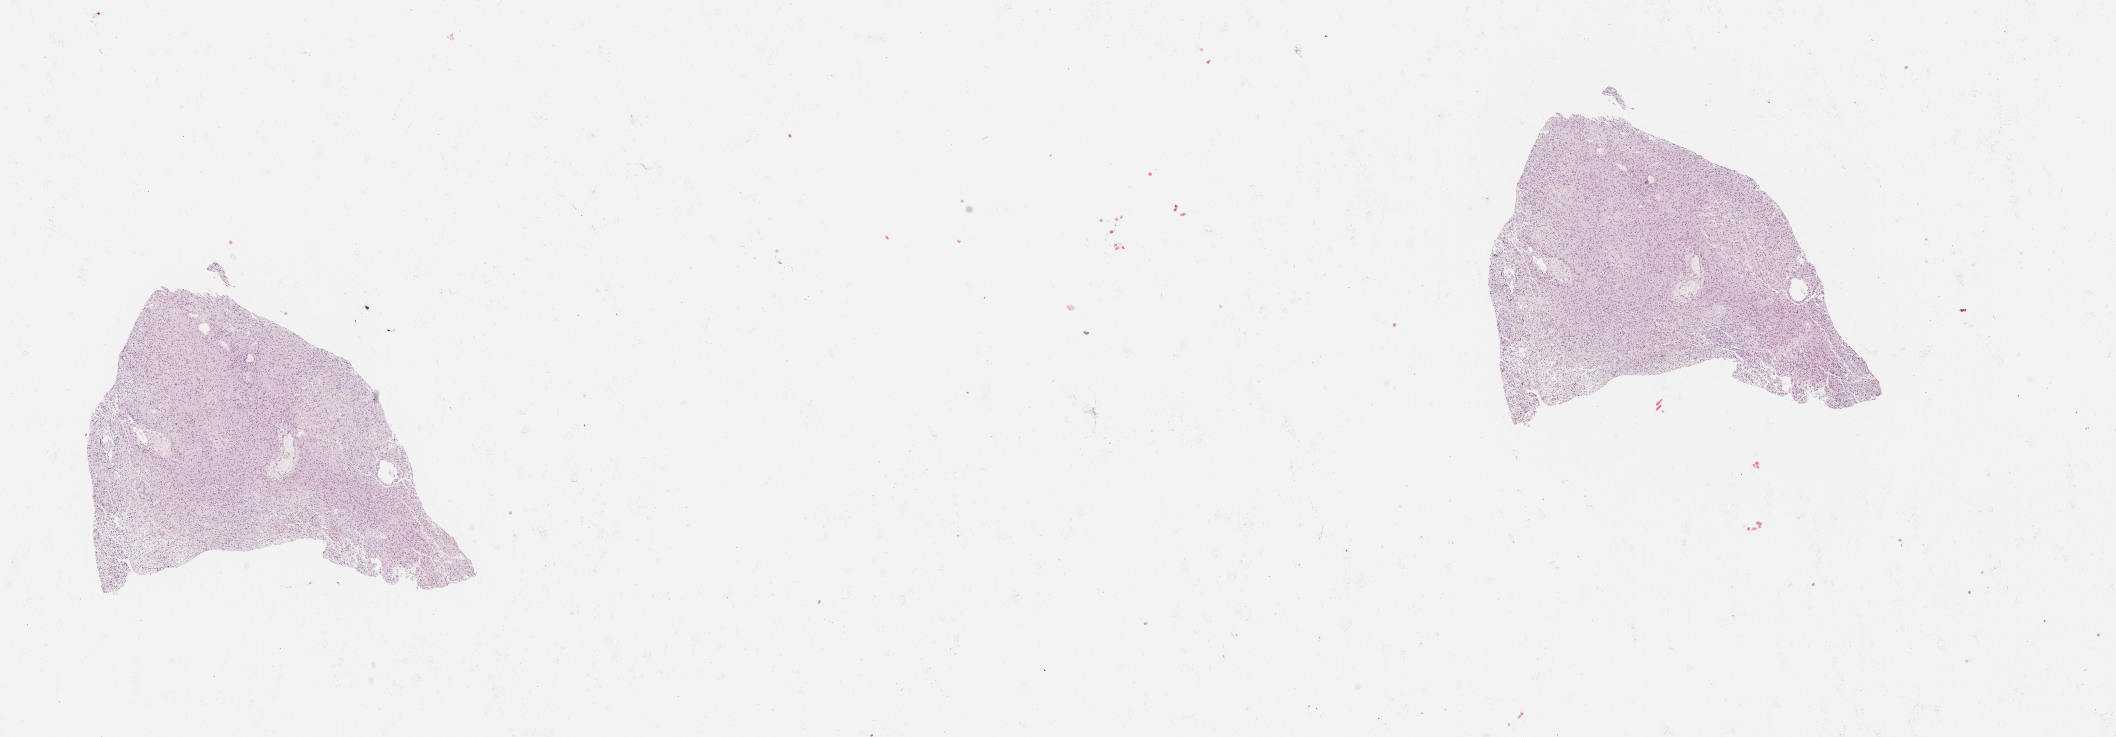
H&E whole-slide image — low-resolution overview of the scanned area, about 17.0 x 5.9 mm. Tumour tissue sample, sampled site: brain. 63-year-old female patient. Slide review estimates, as recorded: tumour nuclei 80%, necrosis 5%.
Primary tumour site (as recorded): temporal lobe. Histologic diagnosis: Glioblastoma.